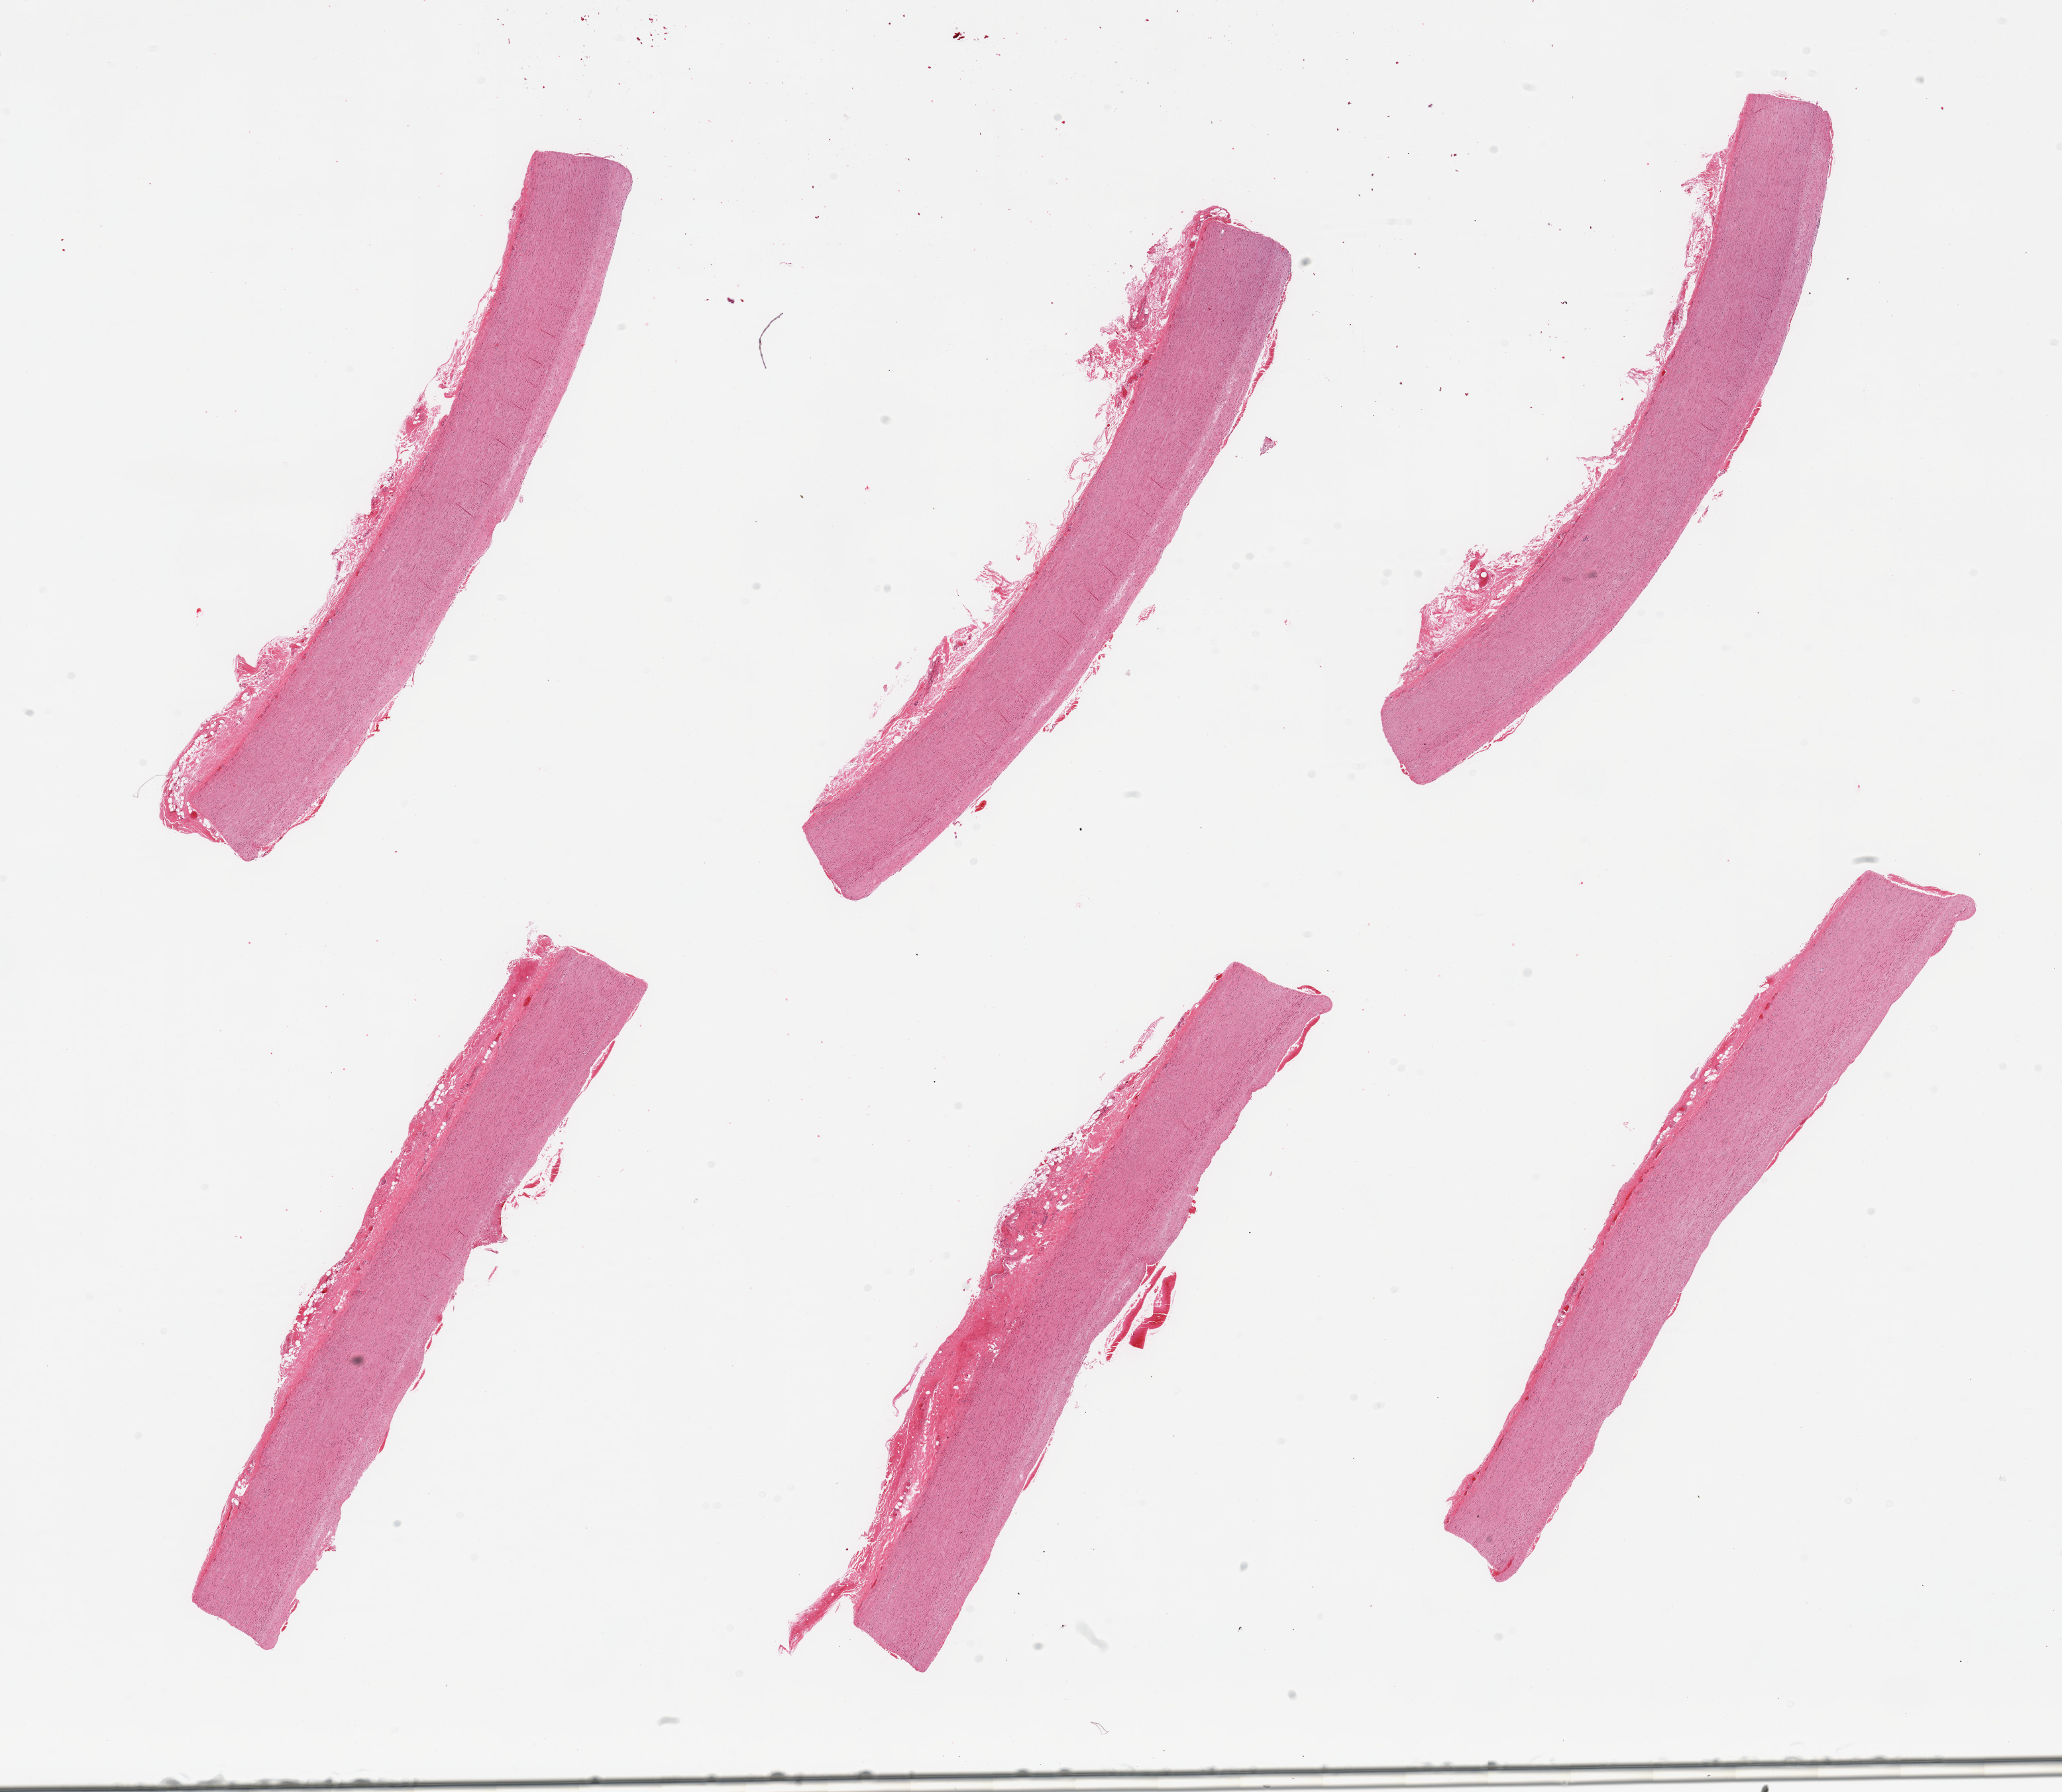
Hematoxylin and eosin (H&E) whole-slide image, shown as a low-resolution overview of the whole scanned area (about 24.6 x 21.4 mm). PAXgene-fixed, paraffin-embedded tissue. Sampled site (target tissue): aorta. Donor tissue sample. Male donor.
Review note (as recorded): 6 pieces, atherosis up to ~0.2mm.